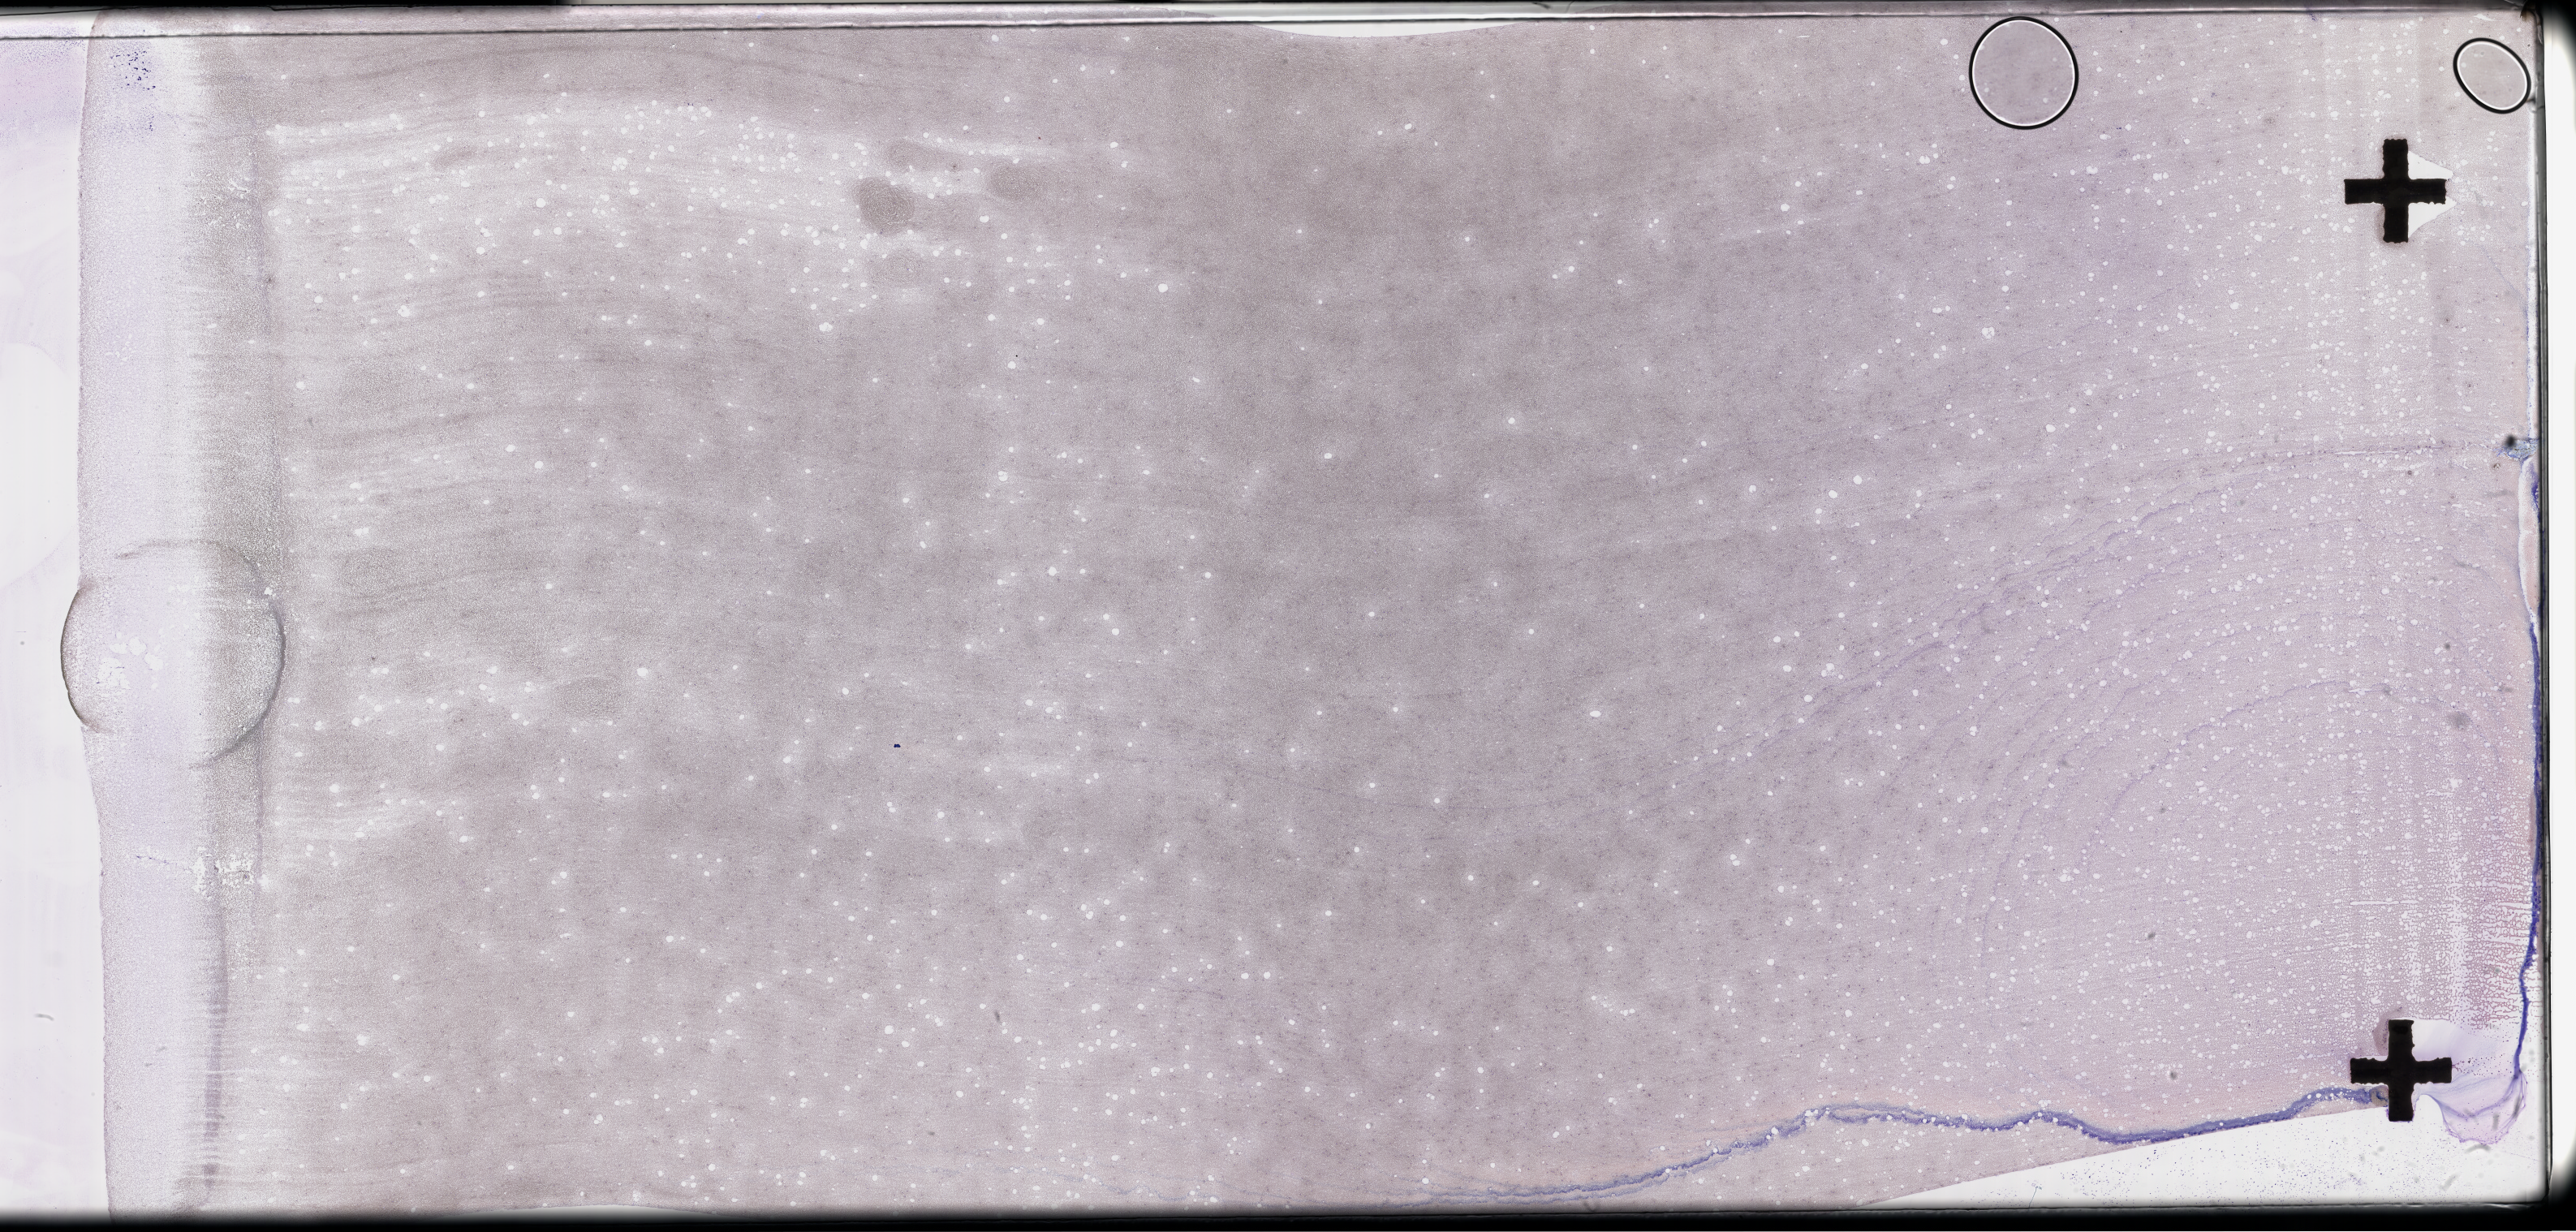
Wright–Giemsa-stained whole blood smear, whole-slide image, a low-resolution overview of the entire scanned area, about 51.3 x 24.5 mm. Patient: male.
Patient diagnosis: Plasma Cell Myeloma.